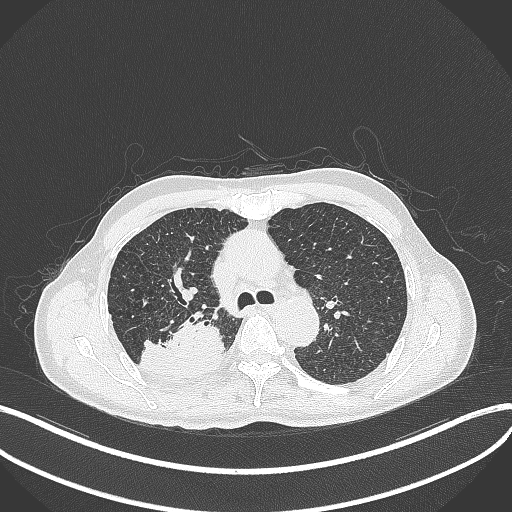
Chest CT, one axial slice; slice 308 of 428 in the series (ordered by position); reconstruction kernel B70f; lung window (W 1500 / L -600 HU); 512 × 512 image matrix, field of view 400 × 400 mm. Male patient, age 79 years. Case-level facts recorded for this patient, not image findings: clinical TNM (as recorded): T3 N0 M0.
Outlined on this slice (rectangle marked by the reading radiologist):
- lung tumour (recorded histology: adenocarcinoma): bounding box (x1, y1, x2, y2) in pixels: (138, 310, 226, 380)